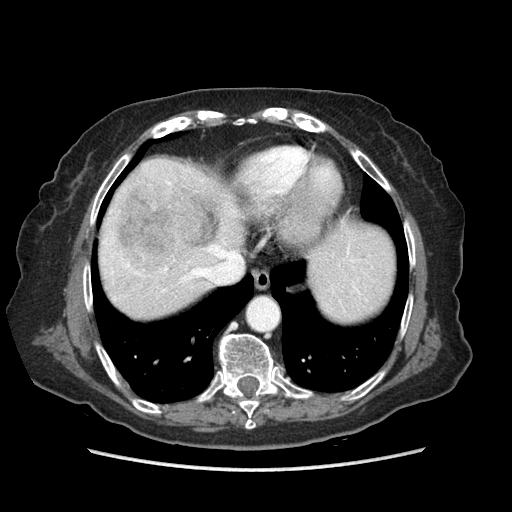
Contrast-enhanced abdominal CT (liver protocol), one axial slice; slice 72 of 89 in the series (ordered by position); soft-tissue window (W 400 / L 40 HU); 2.5 mm slice thickness; 512 × 512 image matrix, field of view 360 × 360 mm. Case-level facts recorded for this patient, not image findings: diagnosis: hepatocellular carcinoma (patient treated with transarterial chemoembolisation; whether this scan precedes or follows treatment is not stated here); TNM stage (as recorded): Stage-IIIA; Child-Pugh class: A; tumour size: 11 cm.
Annotated regions visible in this slice (semi-automatic segmentation, software-assisted and operator-edited):
- abdominal aorta: bounding box (x1, y1, x2, y2) in pixels: (248, 299, 277, 329)
- liver parenchyma outside the tumour (the mass and vessels are separate outlines, so this box may not span the whole liver): (100, 156, 394, 320)
- mass: (119, 183, 220, 281)
- liver vessels: (111, 181, 360, 293)